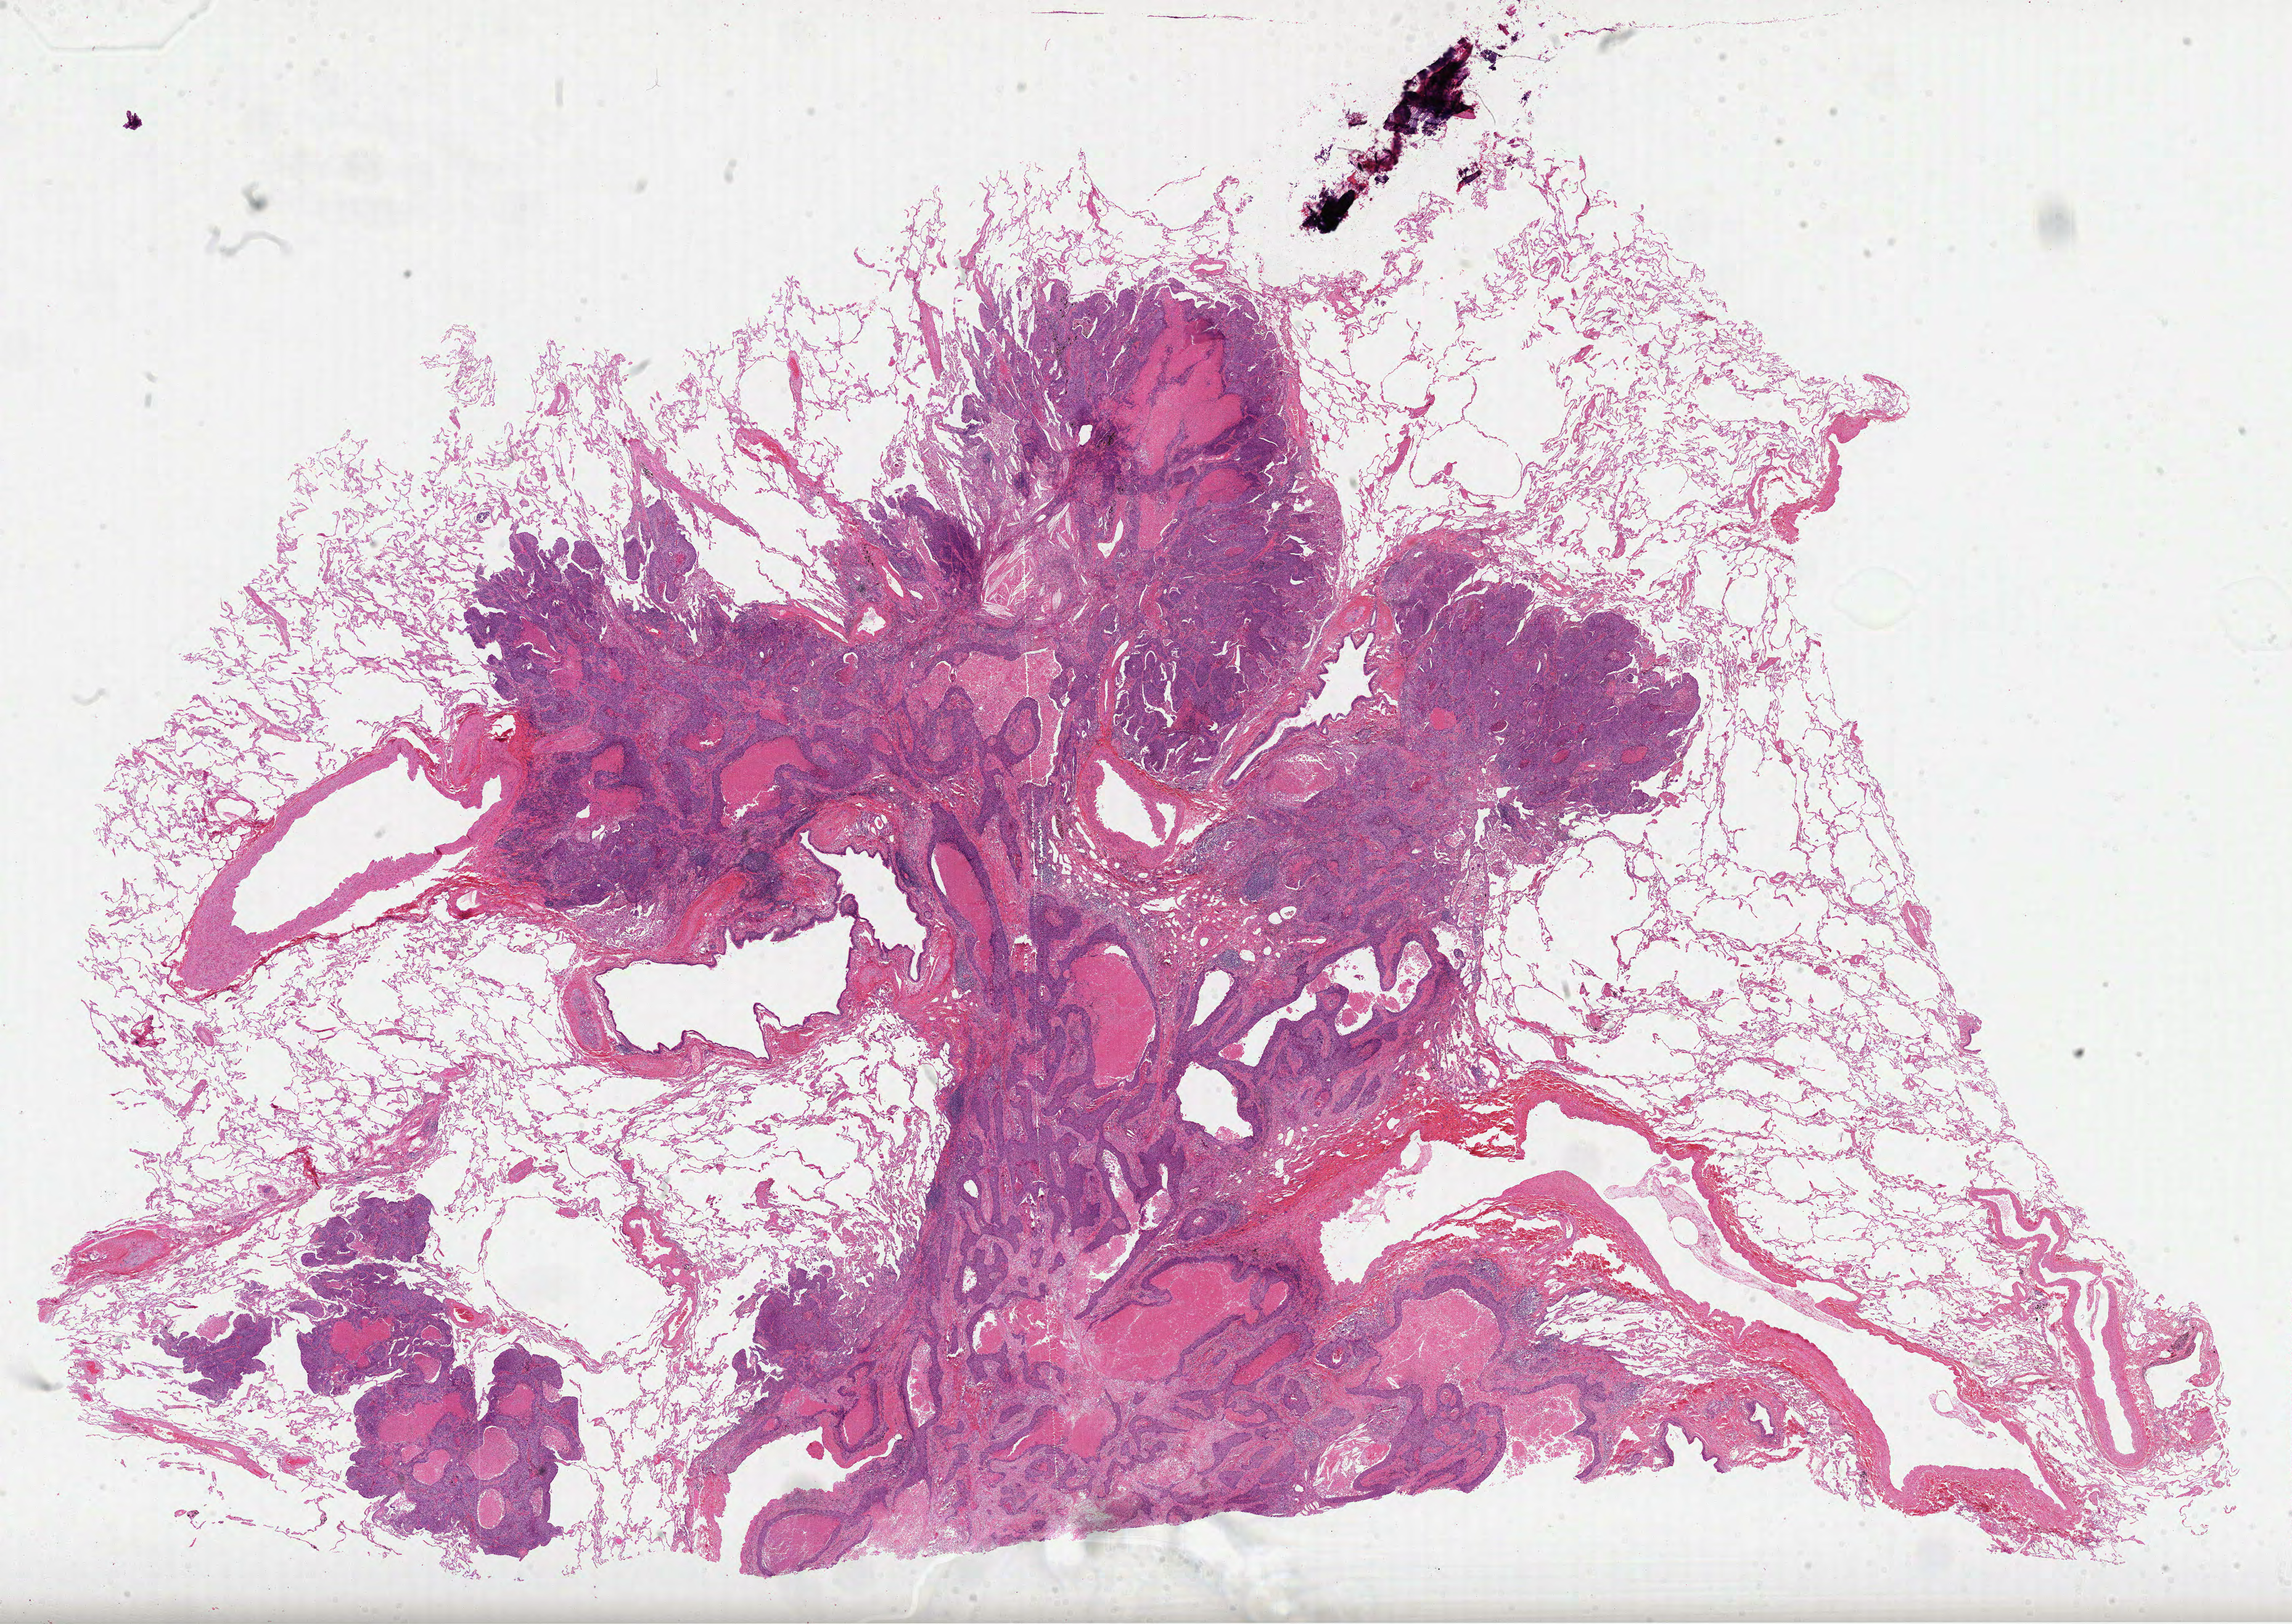
H&E-stained whole-slide image — shown as a low-resolution overview of the whole scanned area (about 30.0 x 21.2 mm, from a 40x scan). Formalin-fixed paraffin-embedded (FFPE) diagnostic section. Sample: primary tumour, lung. Female, age 59 years at initial diagnosis.
TNM: T2 N0 M0. AJCC pathologic stage: IB (6th edition). Diagnosis: Squamous cell carcinoma, NOS.